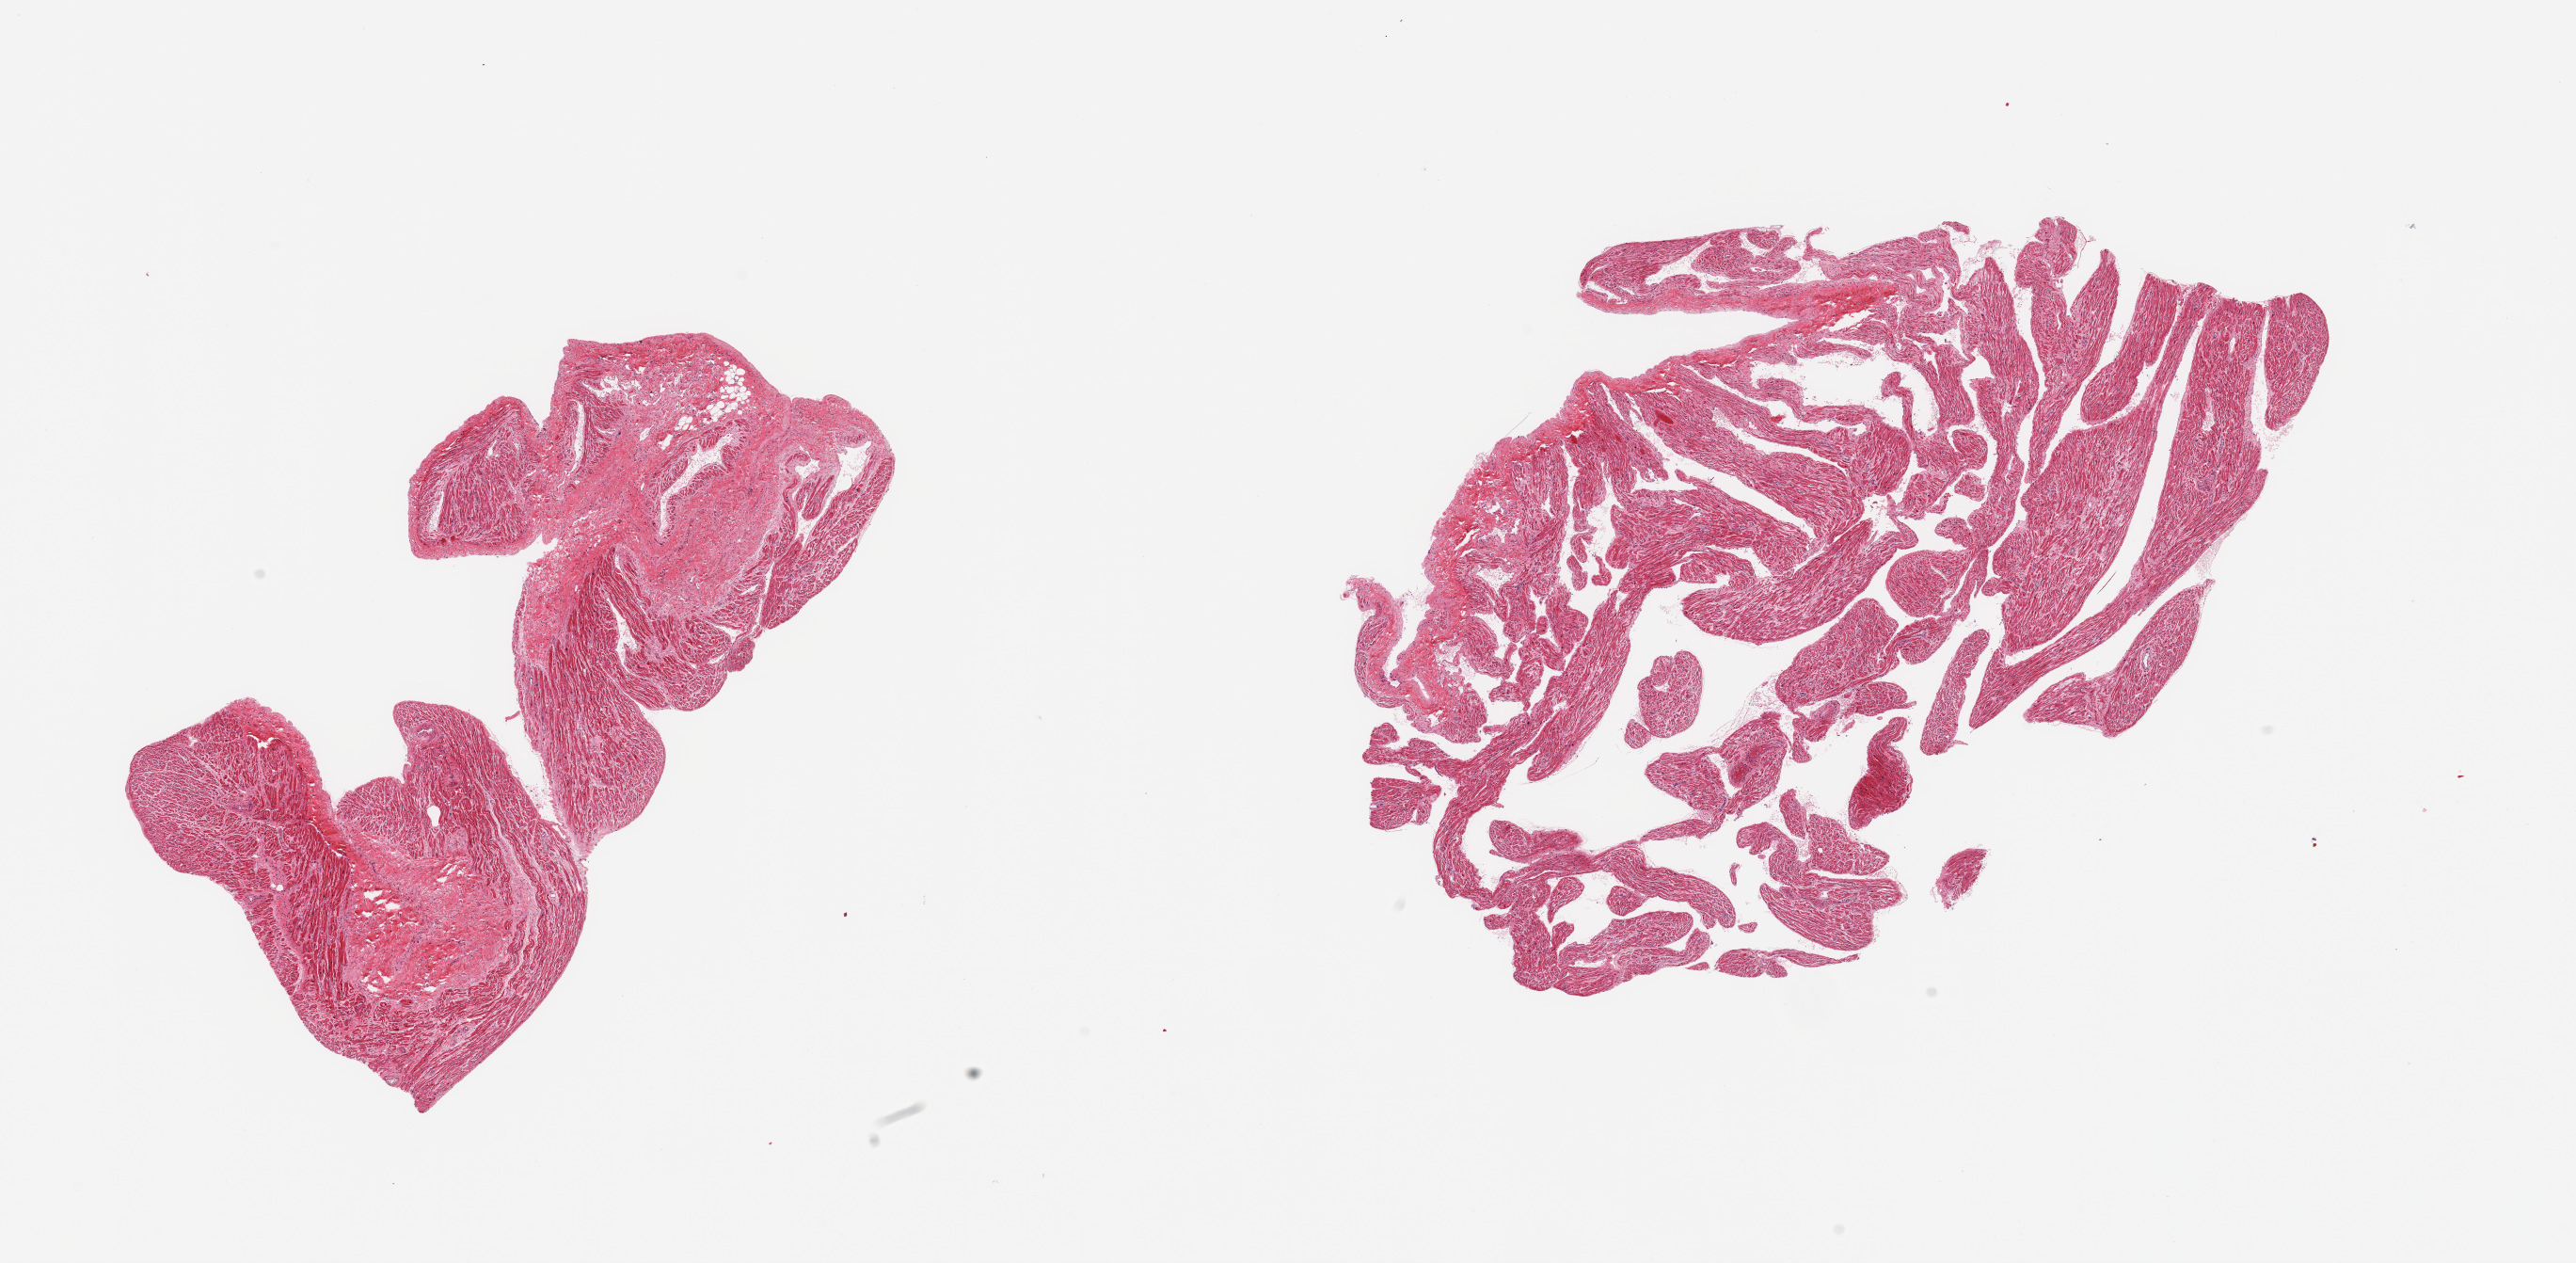
Hematoxylin and eosin (H&E) whole-slide image, brightfield — a low-resolution overview of the entire scanned area, about 21.7 x 10.6 mm. PAXgene-fixed, paraffin-embedded tissue. Sampled site (target tissue): auricular appendage. Tissue donor sample.
Review note (as recorded): 2 pieces; one is ~40% fibrous/fatty.